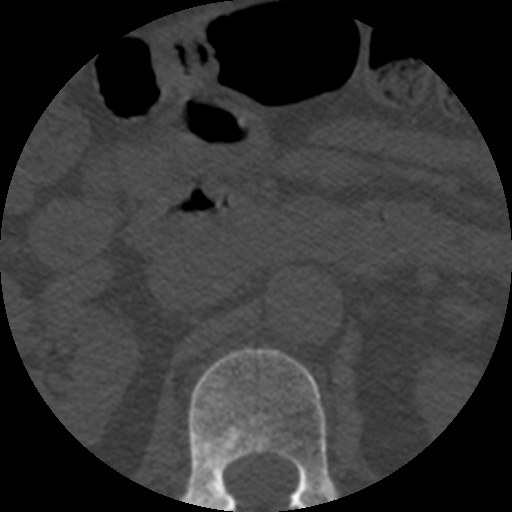
CT including the spine, one axial slice; position 188 of 508 along the scan axis; 120 kVp; bone window (W 1800 / L 400 HU); 1.25 mm slice thickness; 512 × 512 image matrix, field of view 160 × 160 mm. Patient age 57 years. Case-level facts recorded for this patient, not image findings: primary cancer: prostate.
Structures marked on this image (semi-automatic segmentation, software-assisted and operator-edited):
- L1 vertebra: bounding box [x1, y1, x2, y2] px = [180, 348, 337, 512]